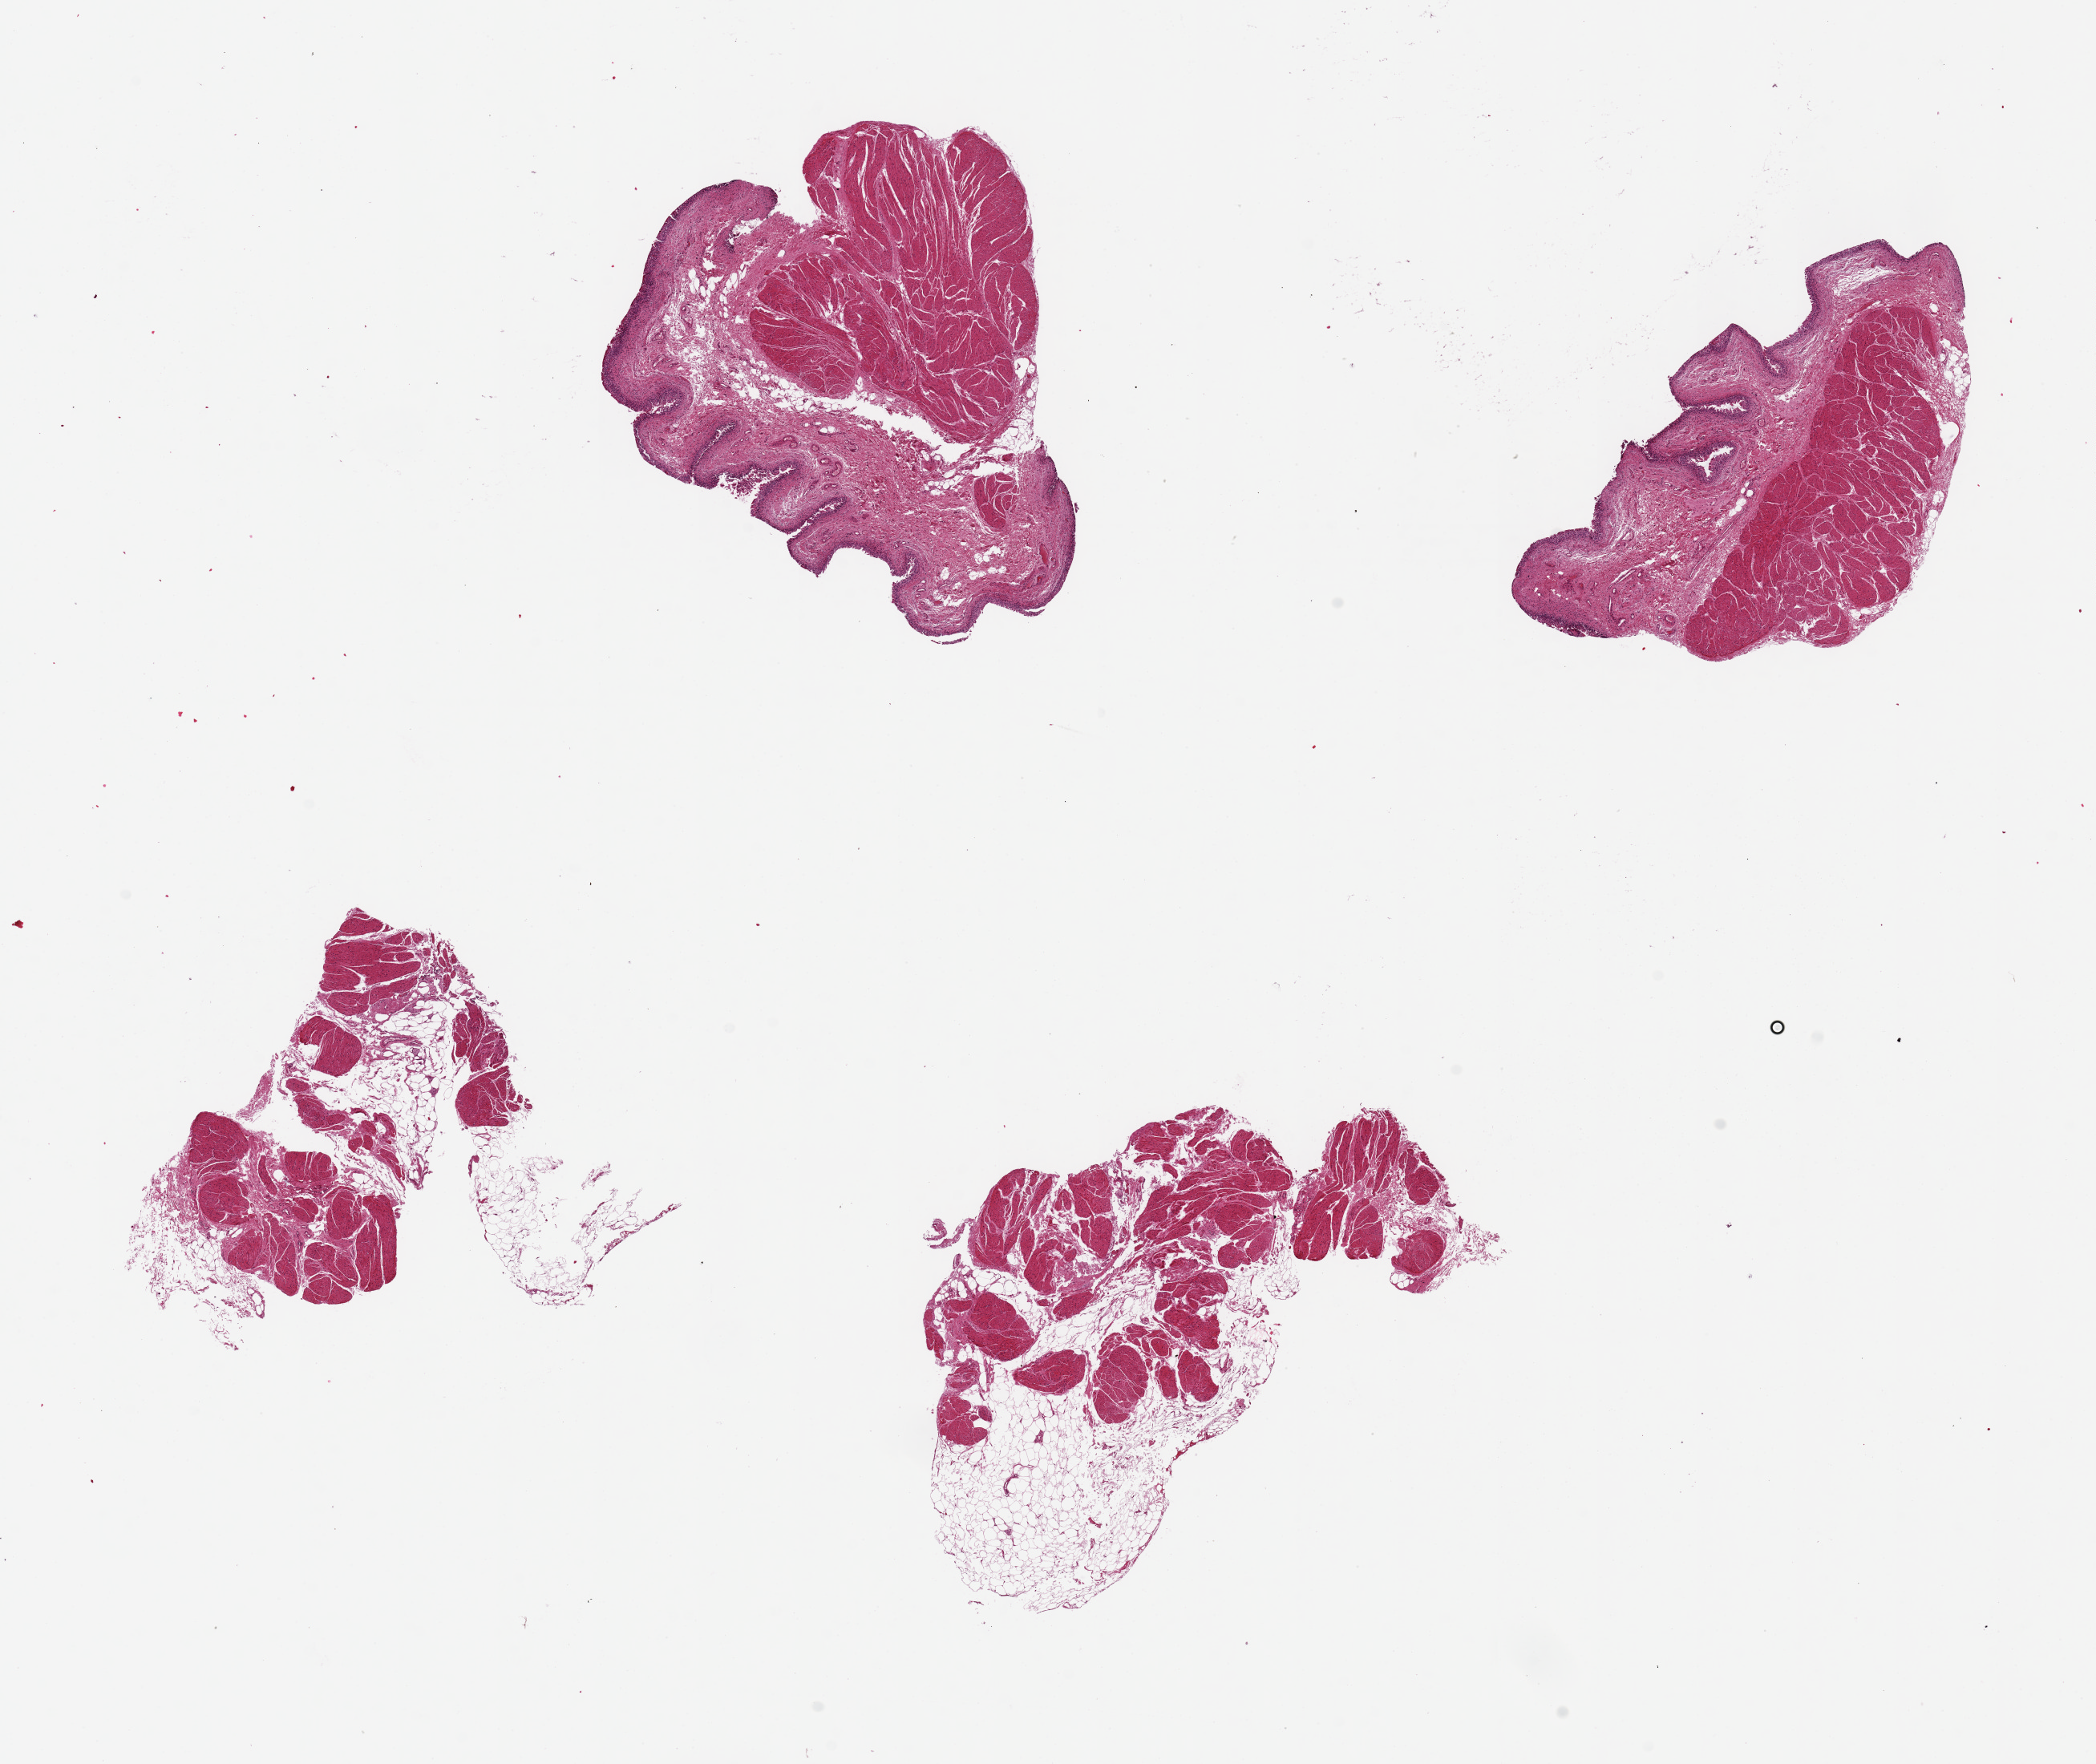
Digitized H&E-stained section, low-resolution overview of the scanned area, about 20.7 x 17.4 mm, PAXgene-fixed paraffin-embedded (PFPE) section, target tissue: urinary bladder, tissue donor sample. Donor: male.
- review note (as recorded): 4 pieces ~5x3mm, 2 with partallly sloughed urothelium, where present <1% of thickness